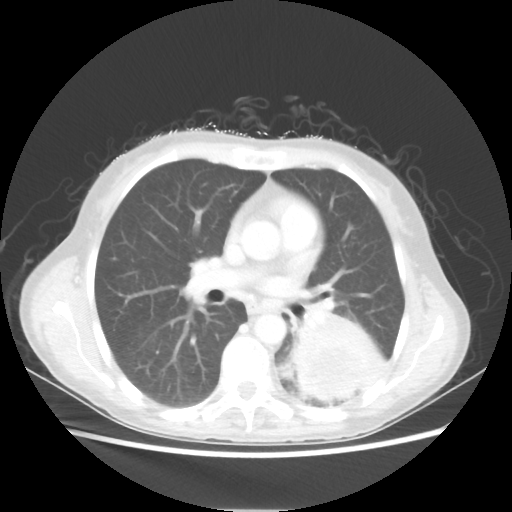
Chest CT, one axial slice. Position 31 of 56 along the scan axis. 80 kVp. Lung window (W 1500 / L -600 HU). 5 mm slice thickness. 512 × 512 image matrix, field of view 360 × 360 mm. Female patient, age 53 years. Case-level facts recorded for this patient, not image findings: clinical TNM (as recorded): T3 N0 M0.
Outlined on this slice (rectangle marked by the reading radiologist):
- lung tumour (recorded histology: adenocarcinoma): box from (x=291, y=300) to (x=386, y=402) px